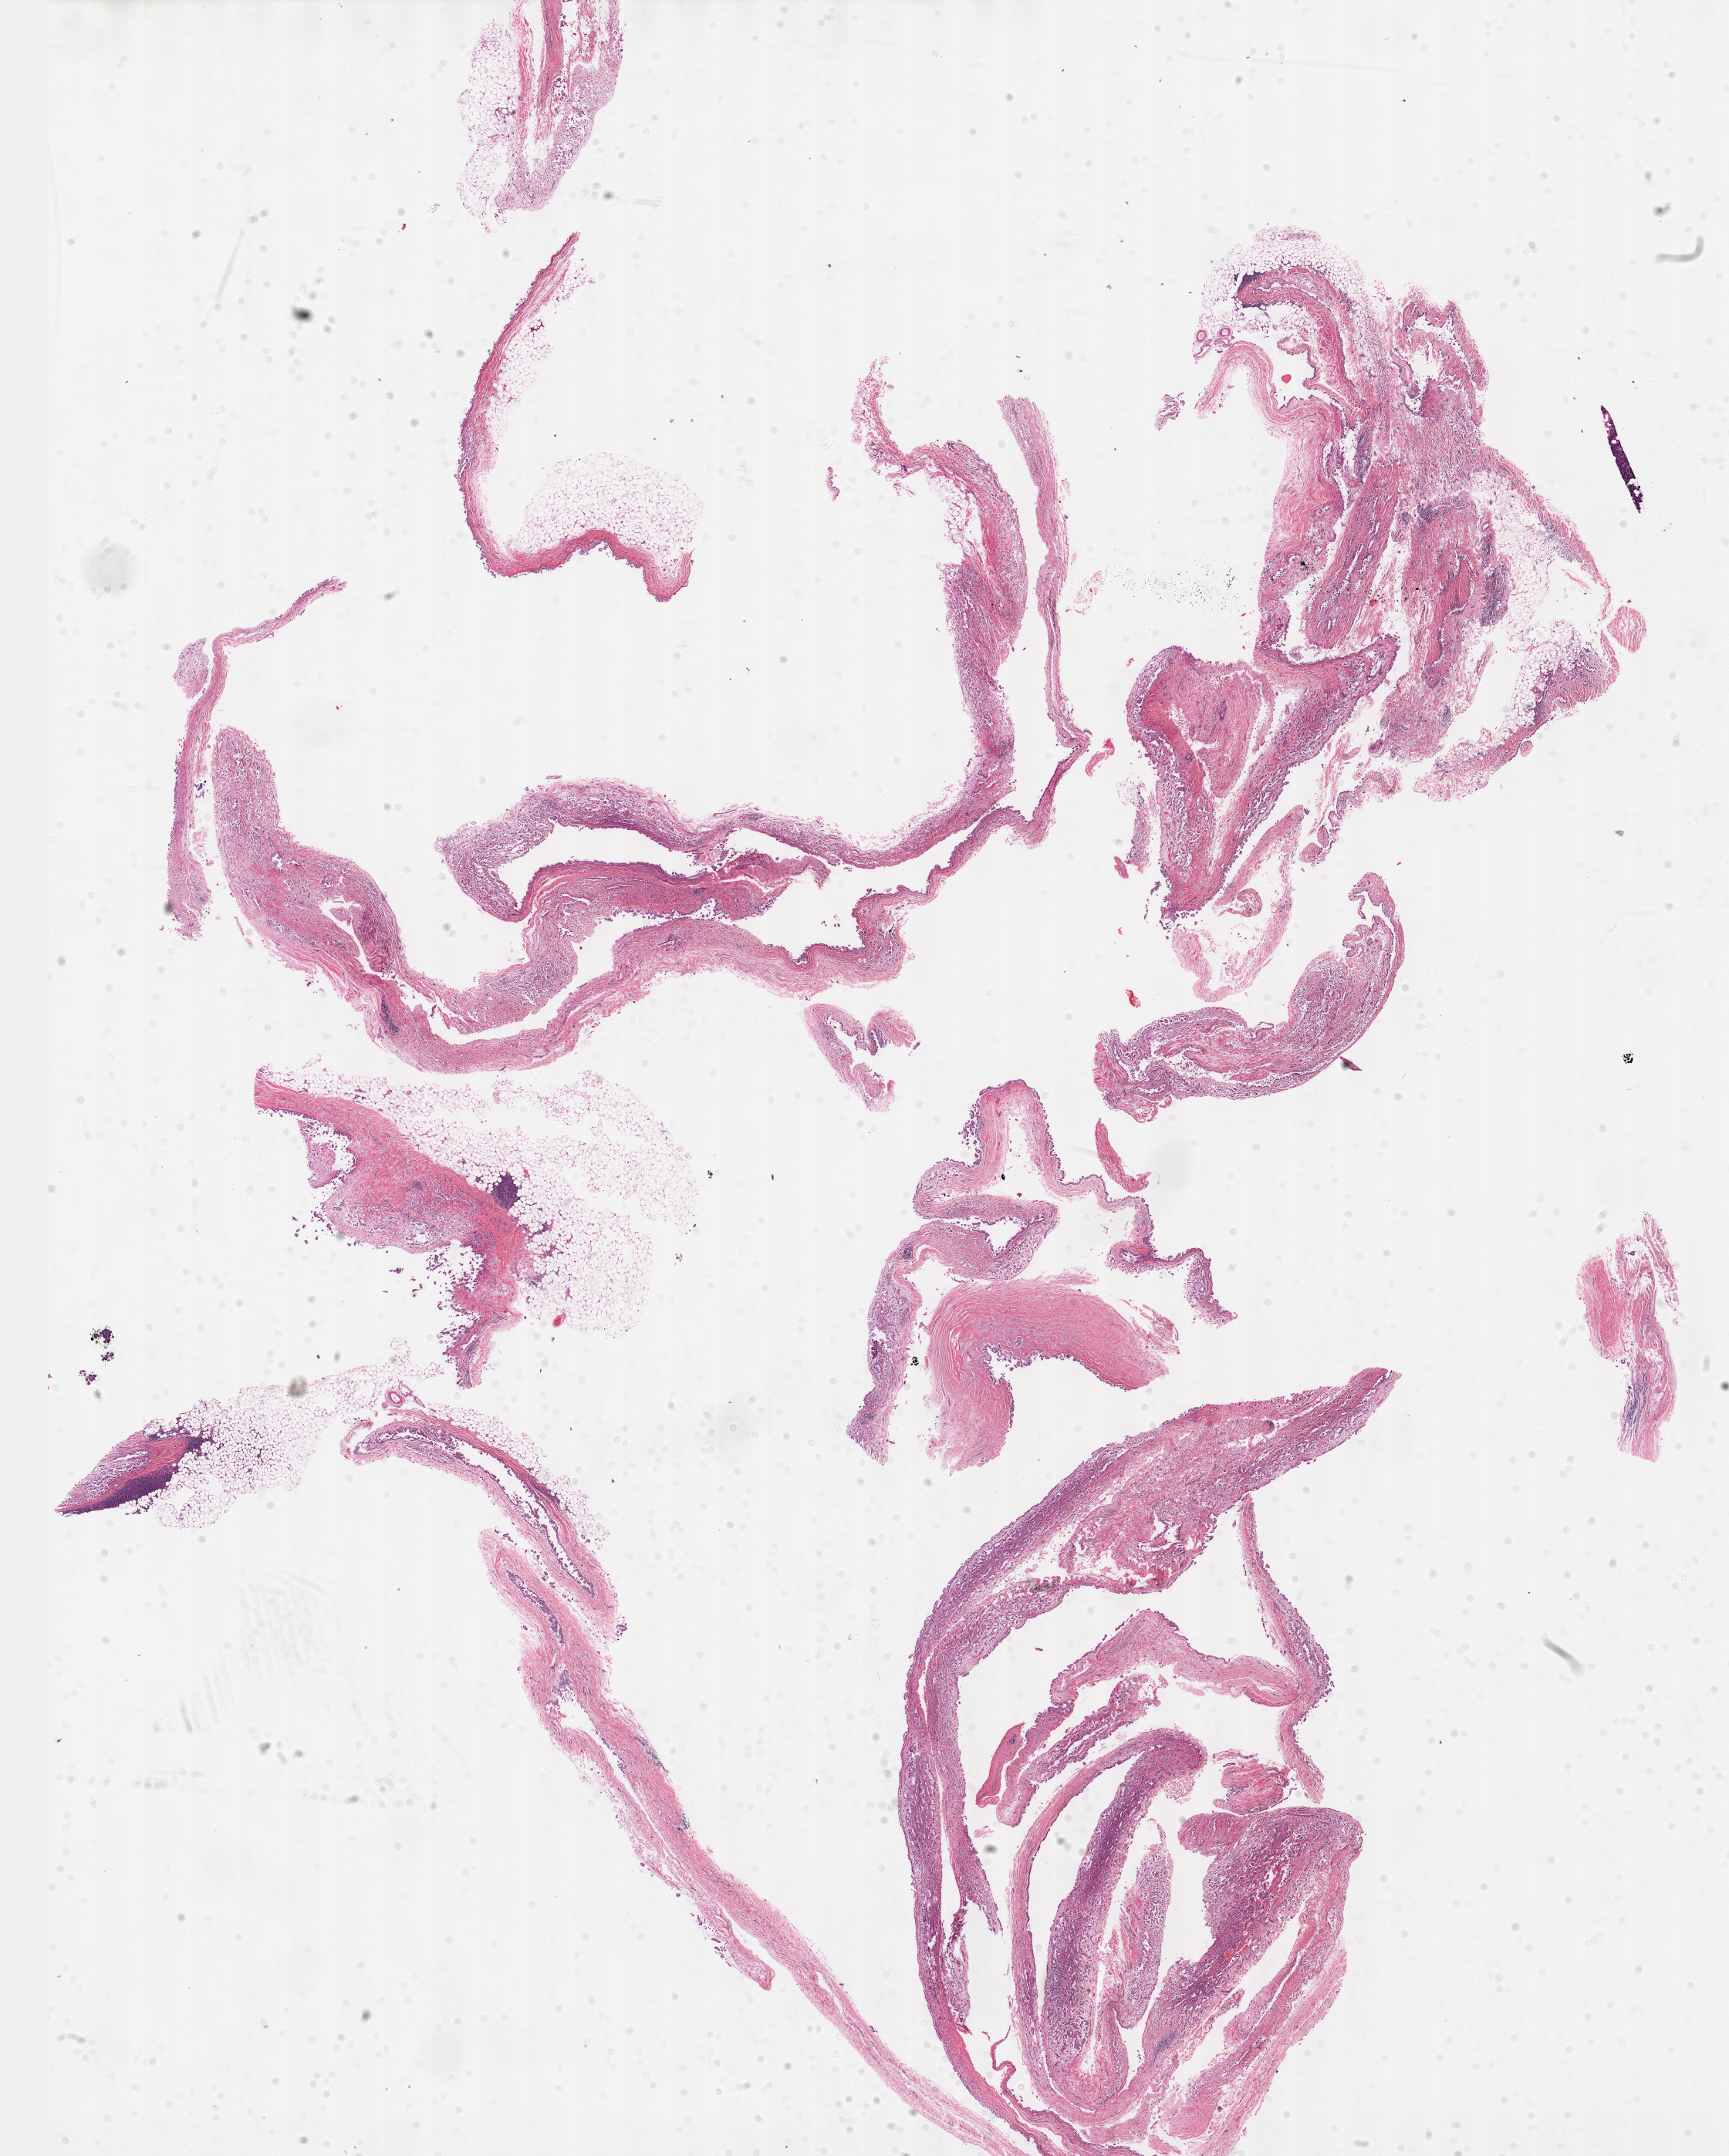
Digitized H&E tissue section (whole slide) — shown as a low-resolution overview of the whole scanned area (about 18.1 x 22.6 mm, from a 40x scan), formalin-fixed paraffin-embedded (FFPE) diagnostic section, sample: primary tumour, mesothelium. Male patient; age at initial diagnosis 62 years.
AJCC pathologic stage: III (7th edition). Laterality: right. Histologic diagnosis: Epithelioid mesothelioma, malignant (pleura, NOS).